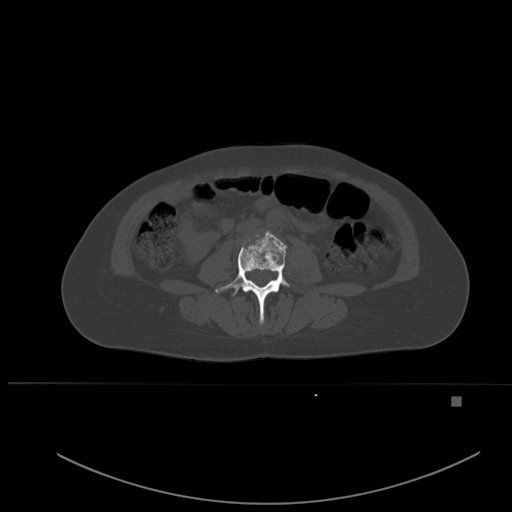
CT including the spine, one axial slice; position 192 of 651 along the scan axis; bone window (W 1800 / L 400 HU); 1.5 mm slice thickness; 512 × 512 image matrix, field of view 443 × 443 mm. Female patient, age 49 years. From the clinical record (not read from this slice): primary cancer: breast; vertebrae with lytic lesions (as recorded): L3, T12, L4.
Annotated regions visible in this slice (semi-automatically segmented with operator editing):
- L3 vertebra: bounding box (x1, y1, x2, y2) in pixels: (215, 231, 290, 324)